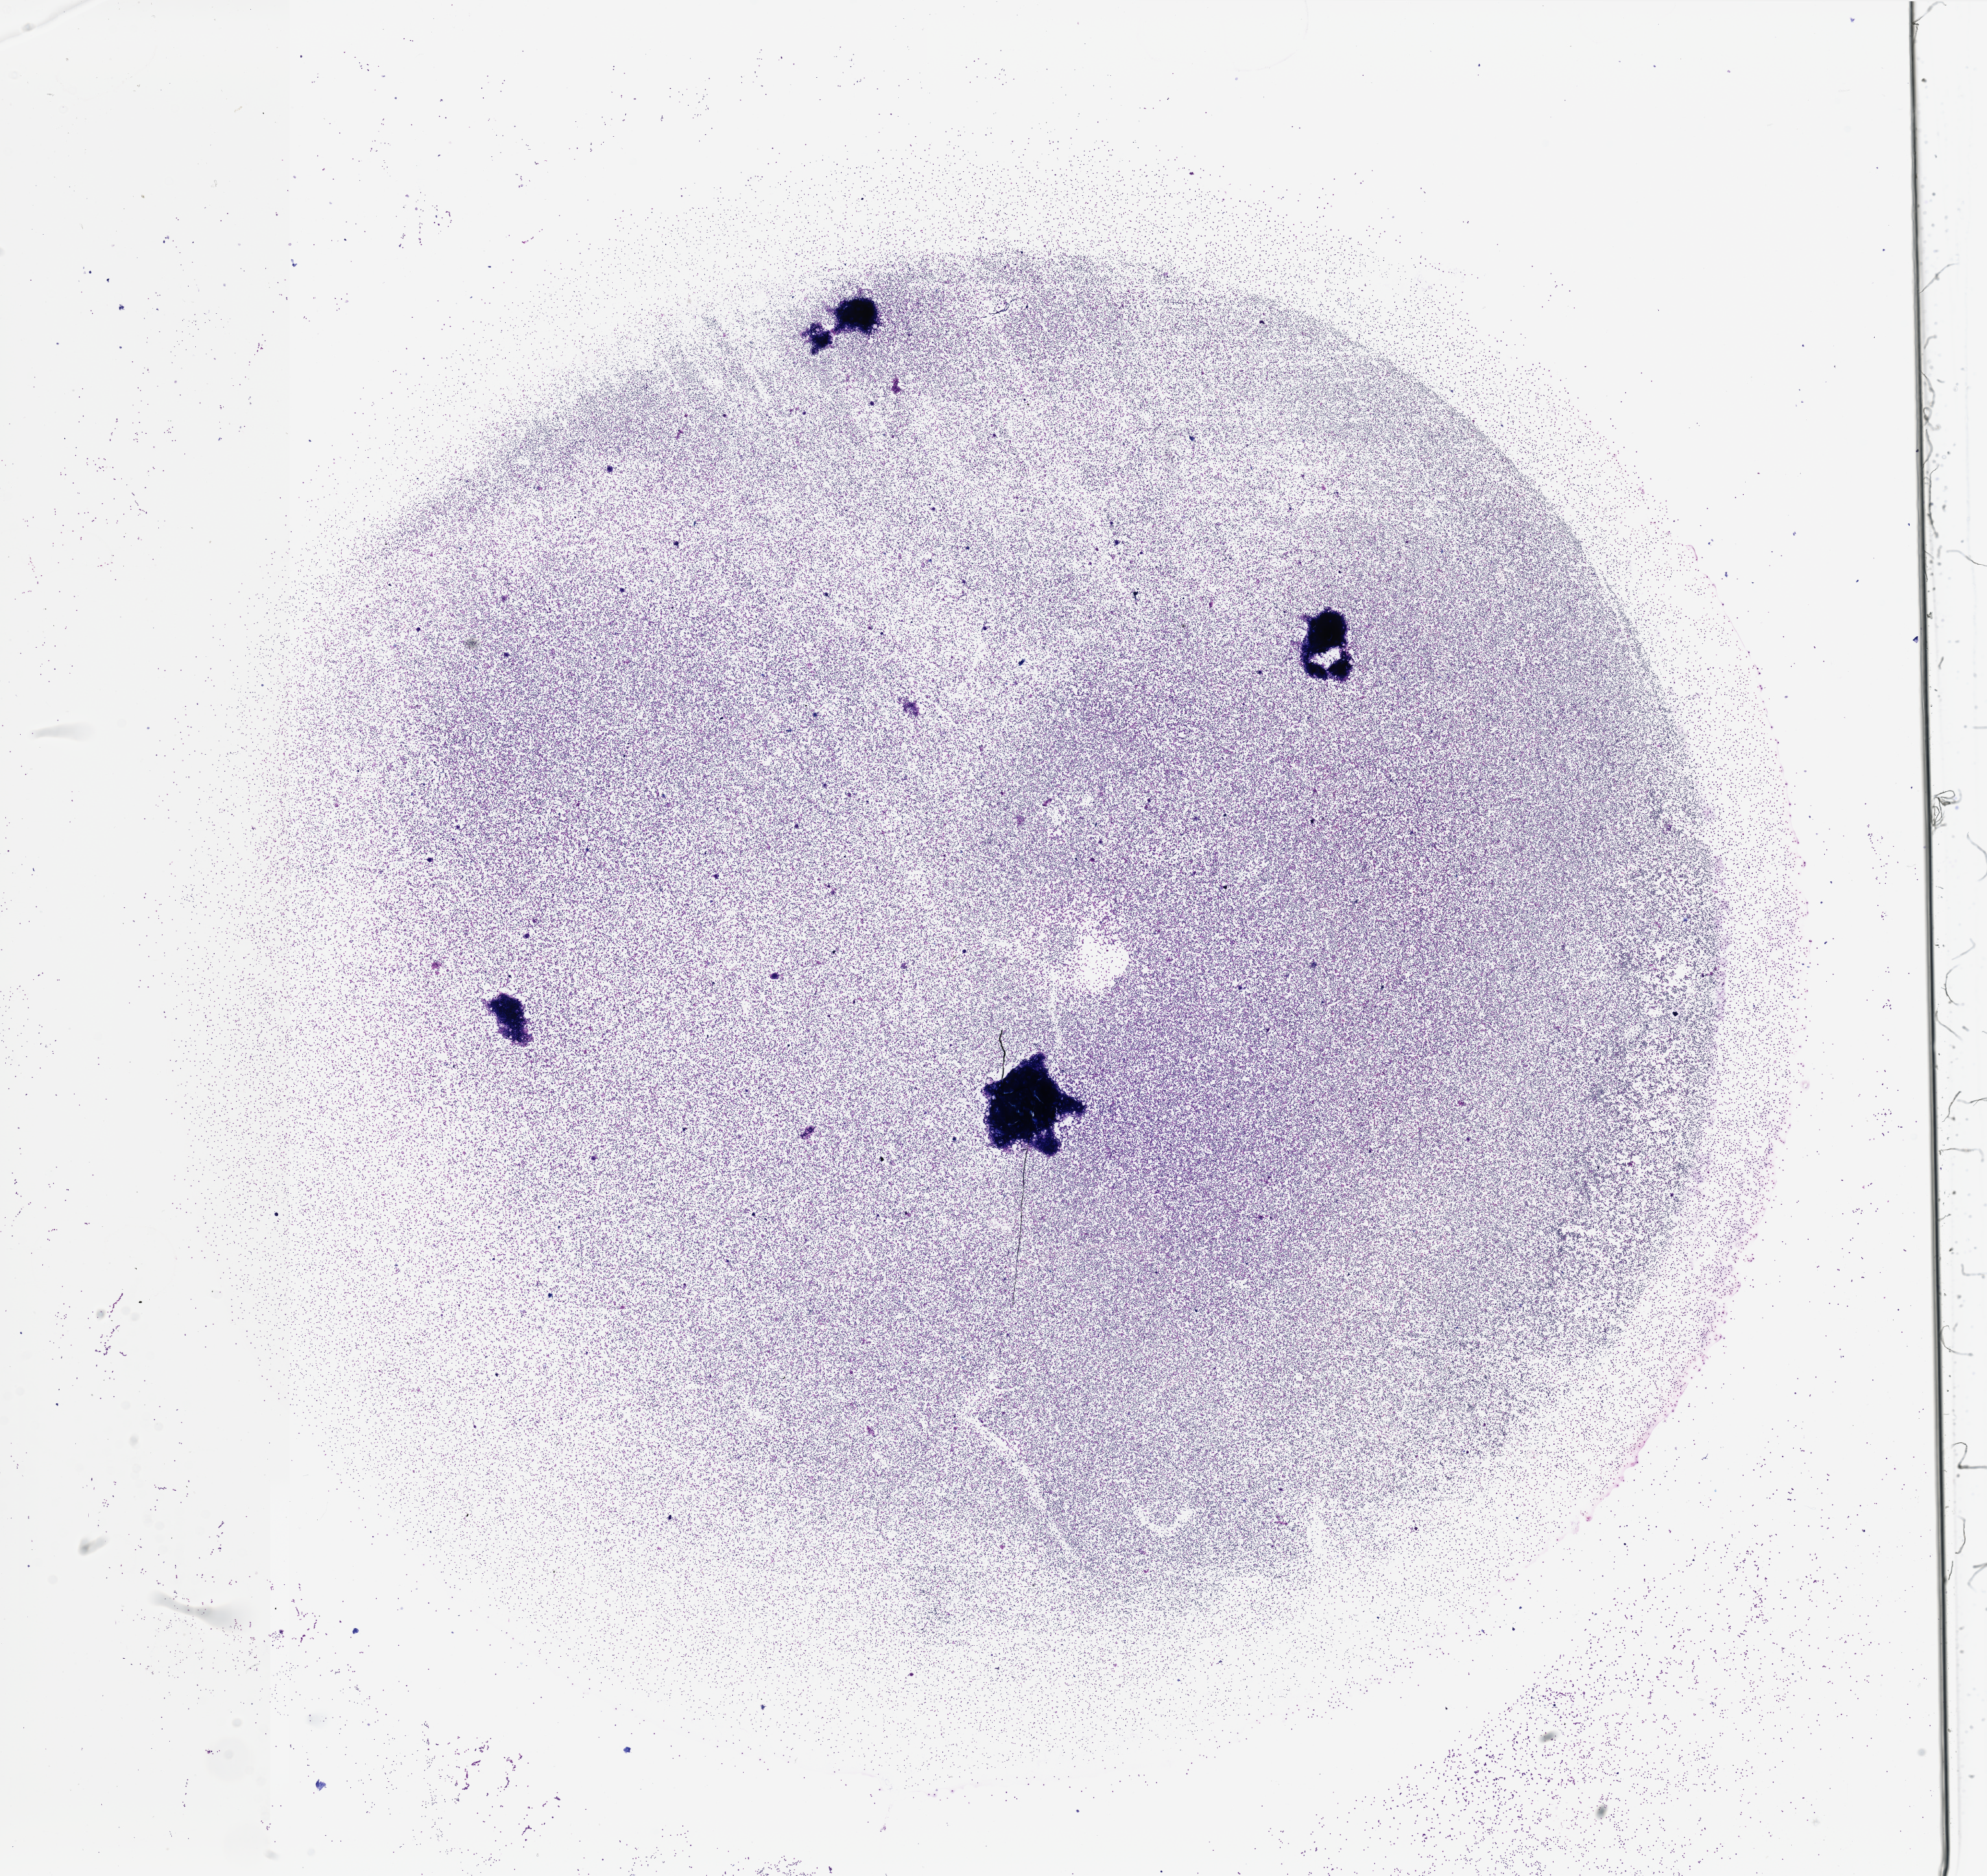
Digitized H&E tissue section (whole slide), shown as a low-resolution overview of the whole scanned area (about 24.2 x 22.8 mm, acquisition: 40x scan), bone marrow (leukaemic) sample. Patient: female, age 65 years. Blasts: 95%.
FAB classification: M5. Diagnosis: Acute Myeloid Leukemia. WHO classification: Acute monoblastic and monocytic leukemia.